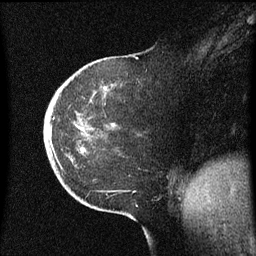
Breast MRI (dynamic contrast-enhanced), one sagittal slice; position 18 of 60 along the scan axis; dynamic contrast-enhanced series, image 2 of 3 at this slice position (ordered by acquisition); 1.5 T; TE 4.2 ms, TR 8.4 ms; 2 mm slice thickness; 256 × 256 image matrix. Female patient, age 38 years. Case-level facts recorded for this patient, not image findings: setting: breast cancer imaged before/during neoadjuvant chemotherapy; receptor status: HER2-positive.
Outlined on this slice (semi-automatically segmented with operator editing):
- analysis volume of interest (the breast-tissue region the enhancement analysis was run in; not a lesion): box from (x=44, y=54) to (x=141, y=185) px
- tumour enhancement mask (voxels above the 70 % enhancement threshold inside the analysis volume of interest): (x=50, y=134)–(x=52, y=137)